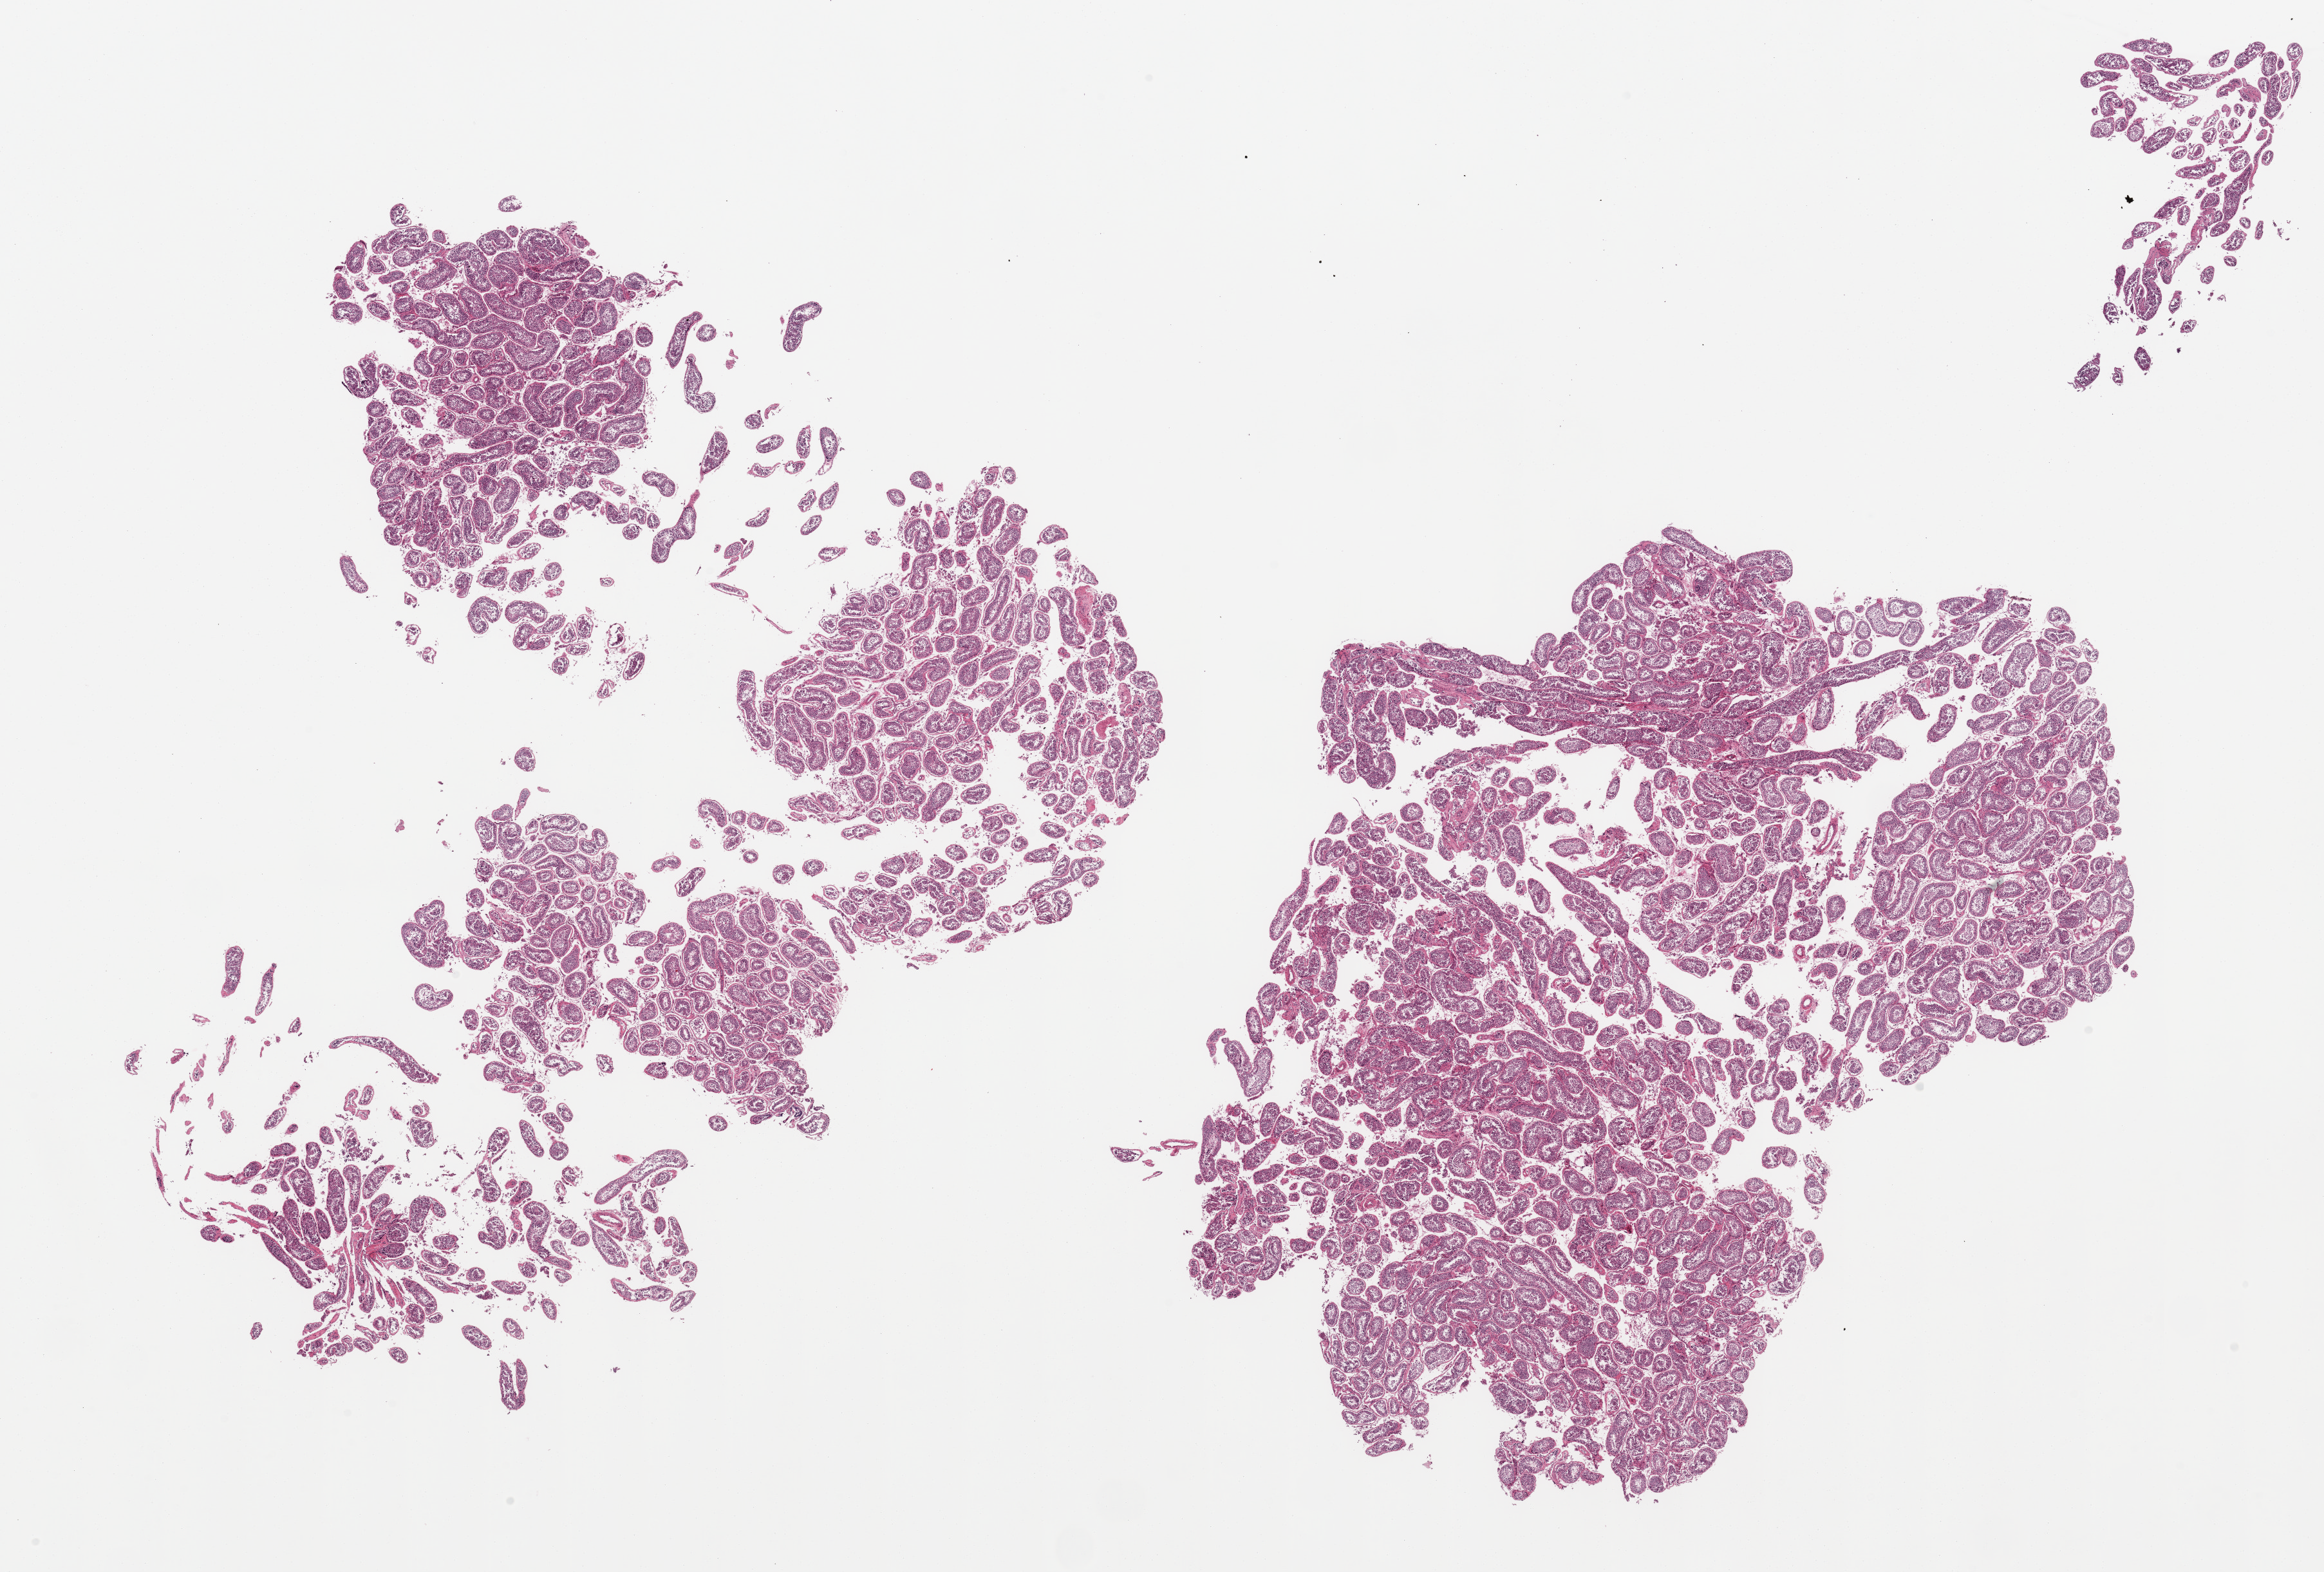
Whole-slide image, hematoxylin and eosin (H&E) stain — low-resolution overview of the scanned area, about 28.5 x 19.3 mm. PAXgene-fixed paraffin-embedded (PFPE) section. Section of testis (target tissue). Tissue donor sample. Donor sex: male.
Reviewer comment on this tissue sample: 2 pieces (fragmented); spermatogenesis is present.